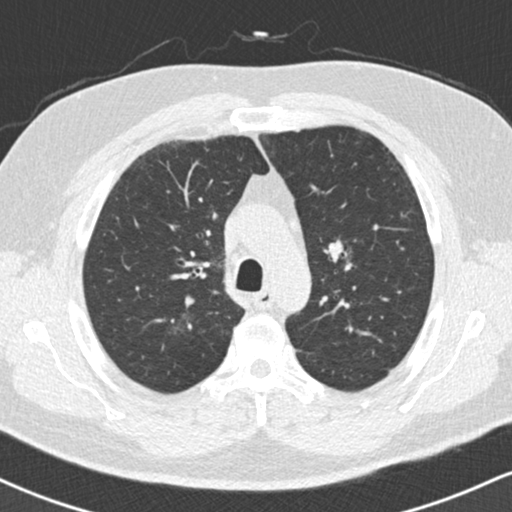
Axial slice from a low-dose chest CT screening exam. Second annual screen. Lung window (W 1500 / L -600 HU). Standard (soft-tissue) reconstruction kernel (B30f). 512 × 512 image matrix. Male, age 59 years at enrolment. Current smoker at enrolment.
Expert-annotated lung lesion, bounding box (x1, y1, x2, y2) in pixels: (153, 299, 210, 360). The exam's reader record, not a measurement of the box and not confirmed to be the same lesion: non-calcified nodule or mass ≥4 mm, right upper lobe, 18 × 16 mm, ground glass attenuation, pre-existing on the prior screen: yes. Participant outcome: lung cancer diagnosed 60 days after this screen — bronchiolo-alveolar adenocarcinoma, NOS, right lower lobe, stage IA (AJCC 6th edition), 15 mm at pathology.